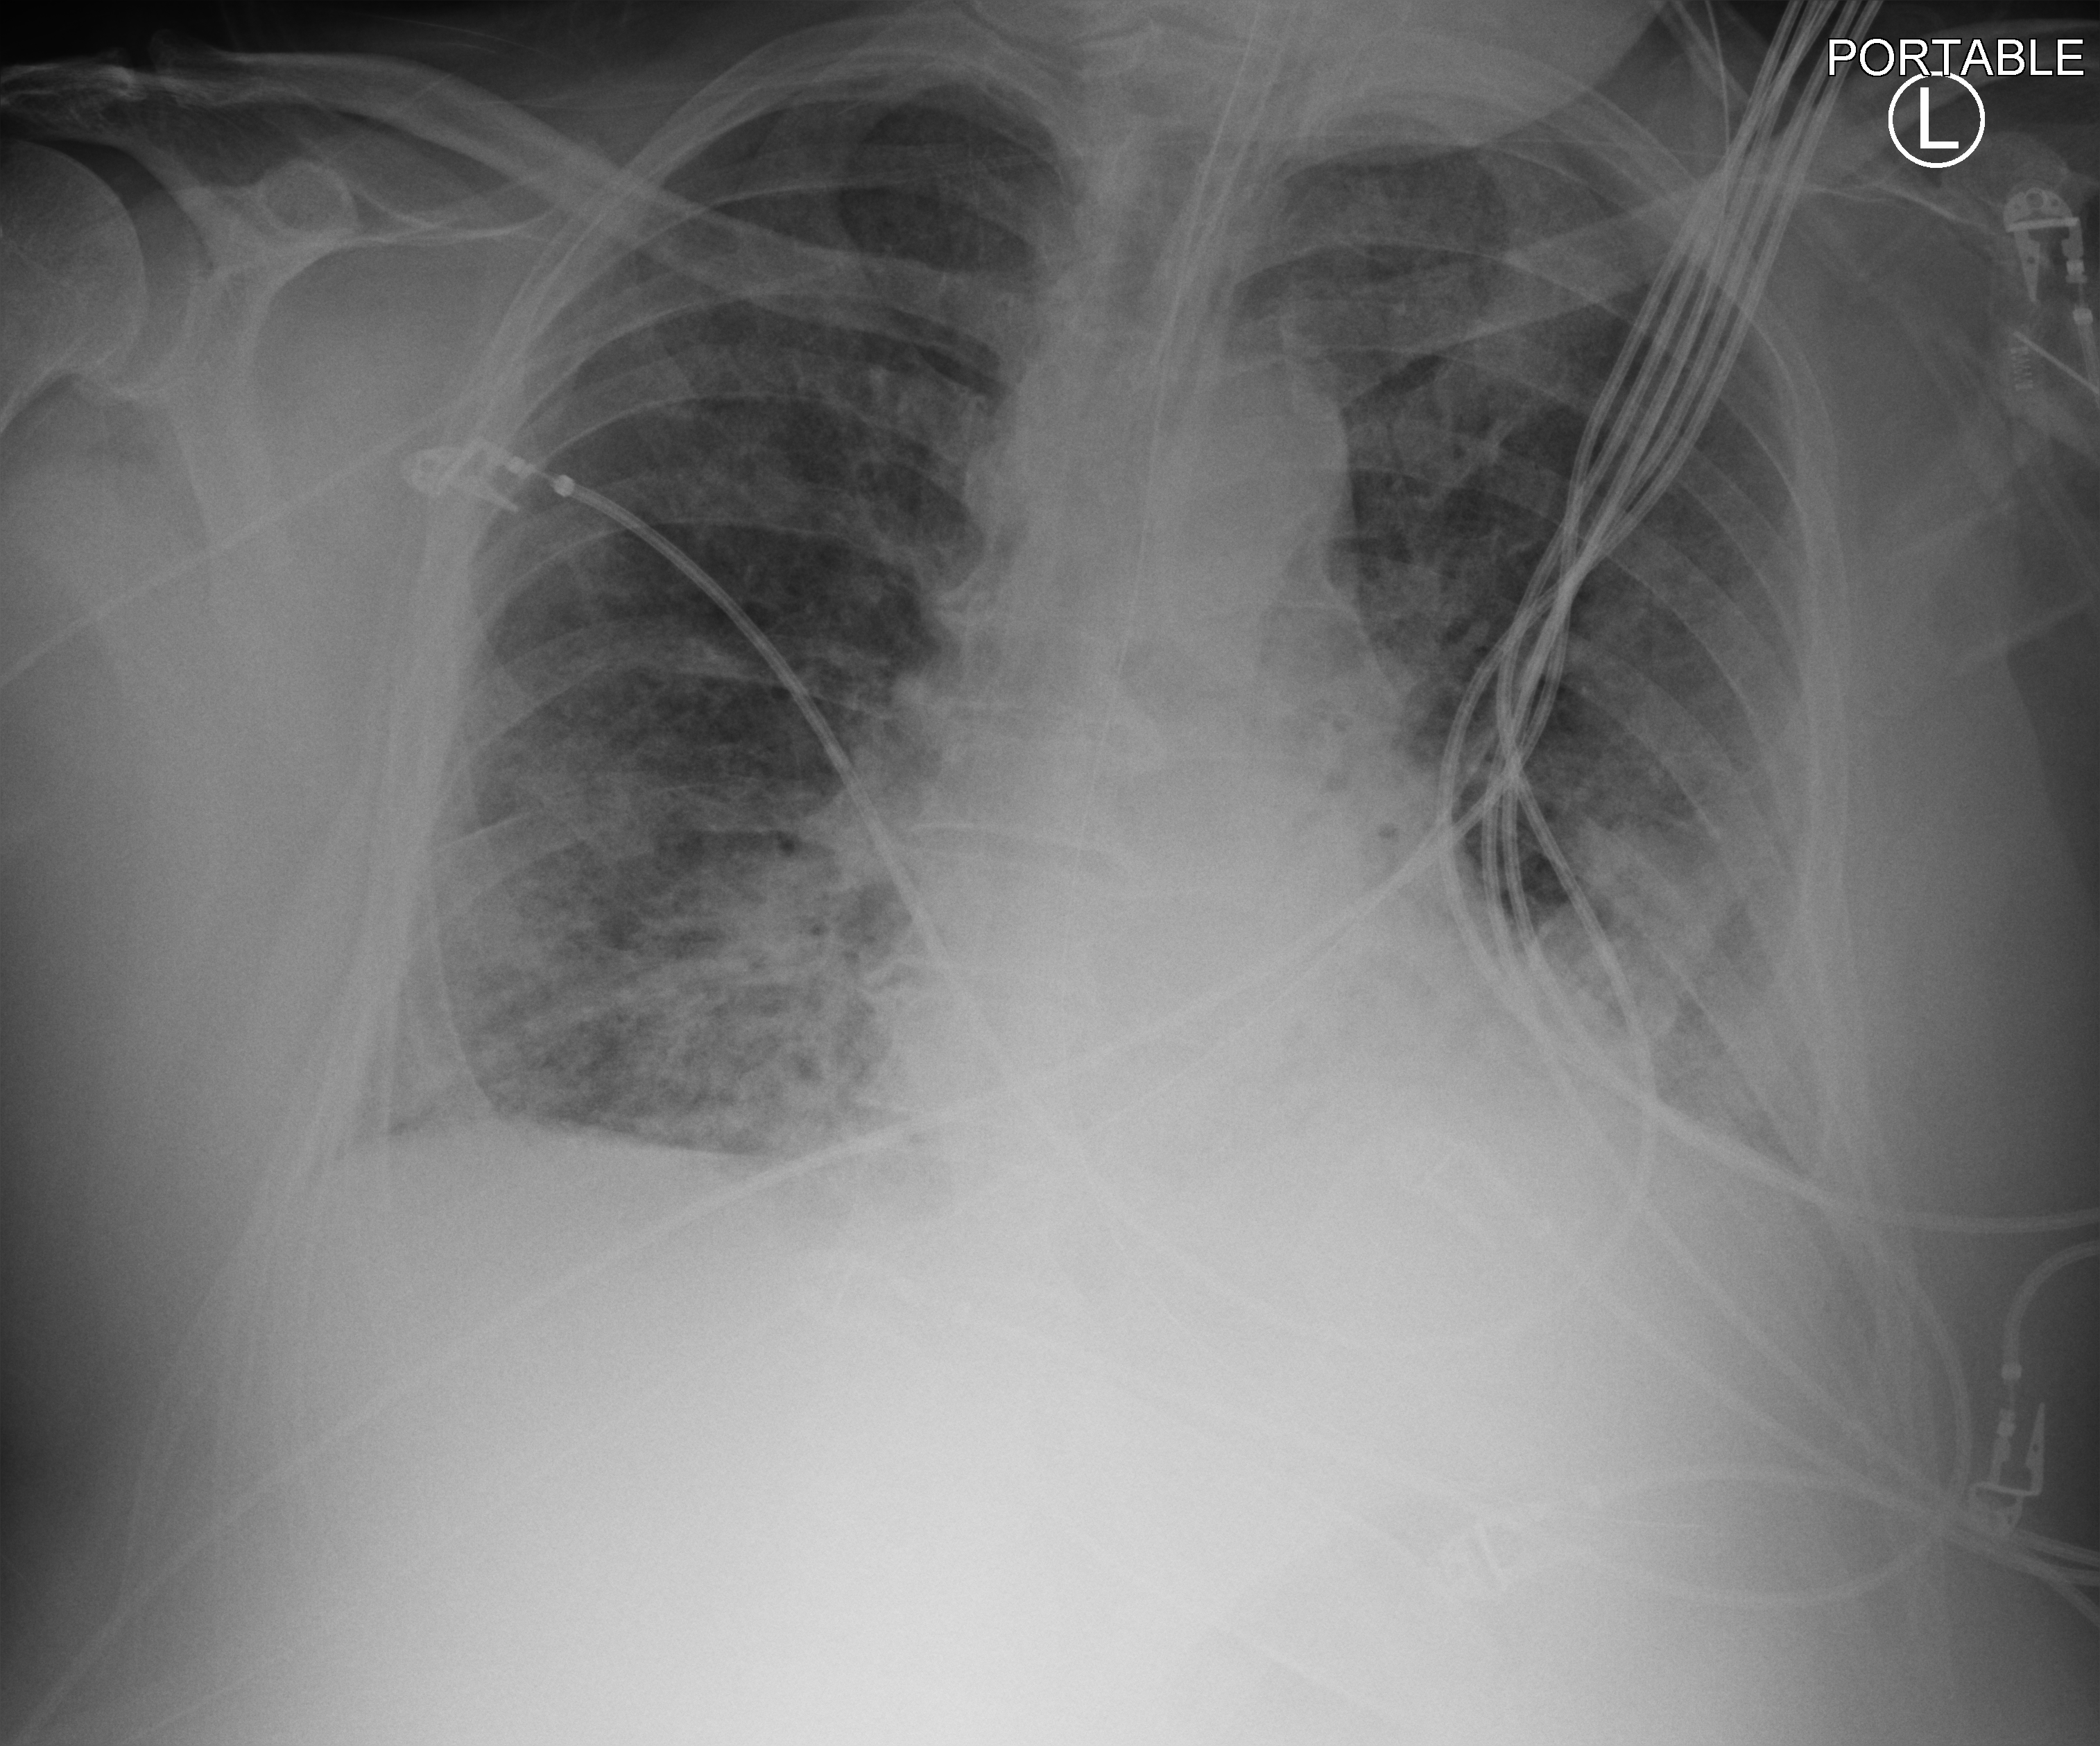
Bedside chest radiograph (computed radiography), anteroposterior (AP) projection. Patient hospitalised with COVID-19; male, aged 60–74 years.
Admission-level facts for this patient (not findings on this image; timing relative to this image not recorded): admitted to intensive care during this hospital stay: yes; mechanically ventilated during this hospital stay: yes.